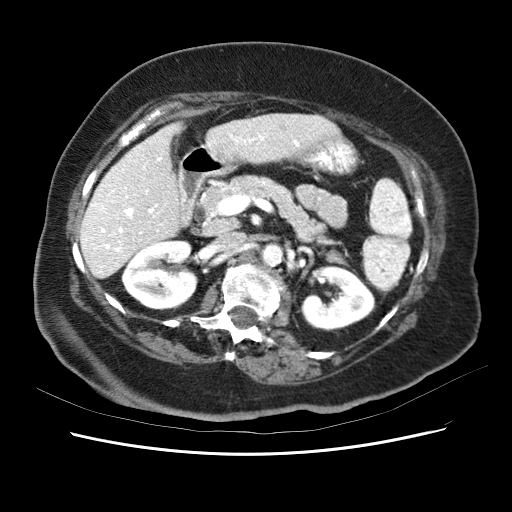
Contrast-enhanced abdominal CT (liver protocol), one axial slice. Position 24 of 62 along the scan axis. Reconstruction kernel STANDARD. Soft-tissue window (W 400 / L 40 HU). 512 × 512 image matrix, field of view 340 × 340 mm. Case-level facts recorded for this patient, not image findings: diagnosis: hepatocellular carcinoma (patient treated with transarterial chemoembolisation; whether this scan precedes or follows treatment is not stated here); TNM stage (as recorded): Stage-I; Child-Pugh class: B; tumour nodularity: uninodular; tumour size: 5.3 cm.
Outlined on this slice (semi-automatically segmented with operator editing):
- liver parenchyma outside the tumour (the mass and vessels are separate outlines, so this box may not span the whole liver): bounding box (x1, y1, x2, y2) in pixels: (80, 110, 346, 278)
- liver vessels: (83, 121, 330, 256)